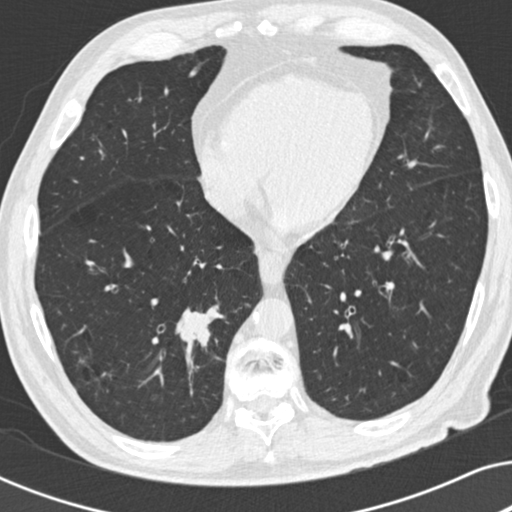
Chest CT (low-dose screening protocol), one axial image, baseline annual screen, lung window (W 1500 / L -600 HU), 2 mm slice thickness, standard (soft-tissue) reconstruction kernel (B30f), 120 kVp. Male, age 73 years at enrolment.
Expert reader's lesion annotation, bounding box [x1, y1, x2, y2] px = [158, 295, 225, 366]. The screening reader recorded 2 non-calcified nodules or masses ≥4 mm on this exam (right lower lobe, right upper lobe); which of them this box marks is not recorded. Official screen result: positive, change unspecified: nodule(s) >= 4 mm or enlarging nodule(s), mass(es), or other non-specific abnormalities suspicious for lung cancer. Participant outcome: lung cancer diagnosed 63 days after this screen — carcinoid tumor, NOS, right lower lobe, carcinoid, stage not assessed, 12 mm at pathology.